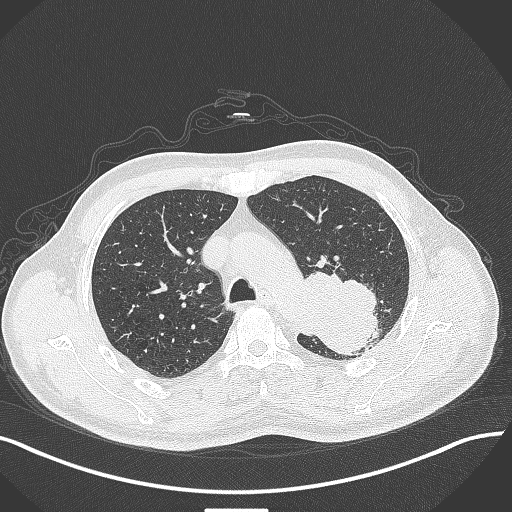
Chest CT, one axial slice. Position 309 of 429 along the scan axis. 120 kVp. Lung window (W 1500 / L -600 HU). 1 mm slice thickness. 512 × 512 image matrix. Patient: male, 55 years. From the clinical record (not read from this slice): clinical TNM (as recorded): T3 N0 M1c.
Structures marked on this image (bounding box drawn by a radiologist):
- lung tumour (recorded histology: adenocarcinoma): box from (x=294, y=268) to (x=380, y=361) px